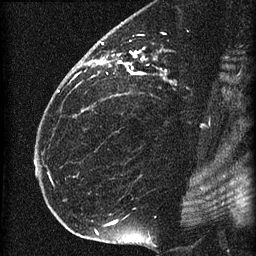
Breast MRI (dynamic contrast-enhanced), one sagittal slice; position 42 of 60 along the scan axis; dynamic contrast-enhanced series, image 2 of 4 at this slice position (ordered by acquisition); 1.5 T; TE 4.2 ms, TR 22.7 ms; 256 × 256 image matrix, field of view 180 × 180 mm. Female patient, age 35 years. From the clinical record (not read from this slice): setting: breast cancer imaged before/during neoadjuvant chemotherapy; receptor status: HR-positive, HER2-negative.
Structures marked on this image (semi-automatically segmented with operator editing):
- analysis volume of interest (the breast-tissue region the enhancement analysis was run in; not a lesion): bounding box (x1, y1, x2, y2) in pixels: (69, 27, 198, 112)
- tumour enhancement mask (voxels above the 90 % enhancement threshold inside the analysis volume of interest): (80, 42, 166, 75)